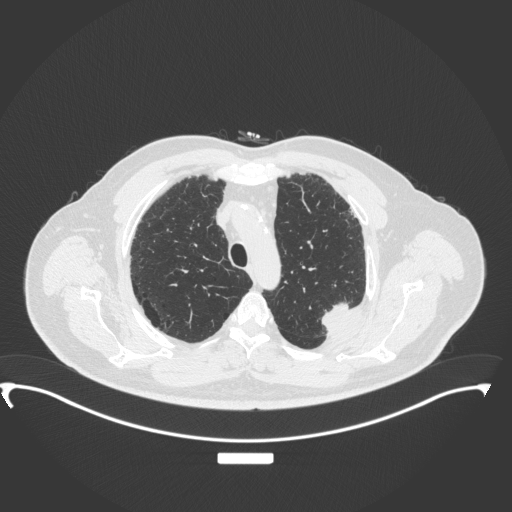
Chest CT, one axial slice; slice 281 of 350 in the series (ordered by position); reconstruction kernel B31f; 120 kVp; lung window (W 1500 / L -600 HU); 1 mm slice thickness; 512 × 512 image matrix, field of view 459 × 459 mm. Patient: male, 64 years. From the clinical record (not read from this slice): clinical TNM (as recorded): T1c N1 M1.
Annotated regions visible in this slice (bounding box drawn by a radiologist):
- lung tumour (recorded histology: adenocarcinoma): bounding box (x1, y1, x2, y2) in pixels: (317, 297, 352, 329)